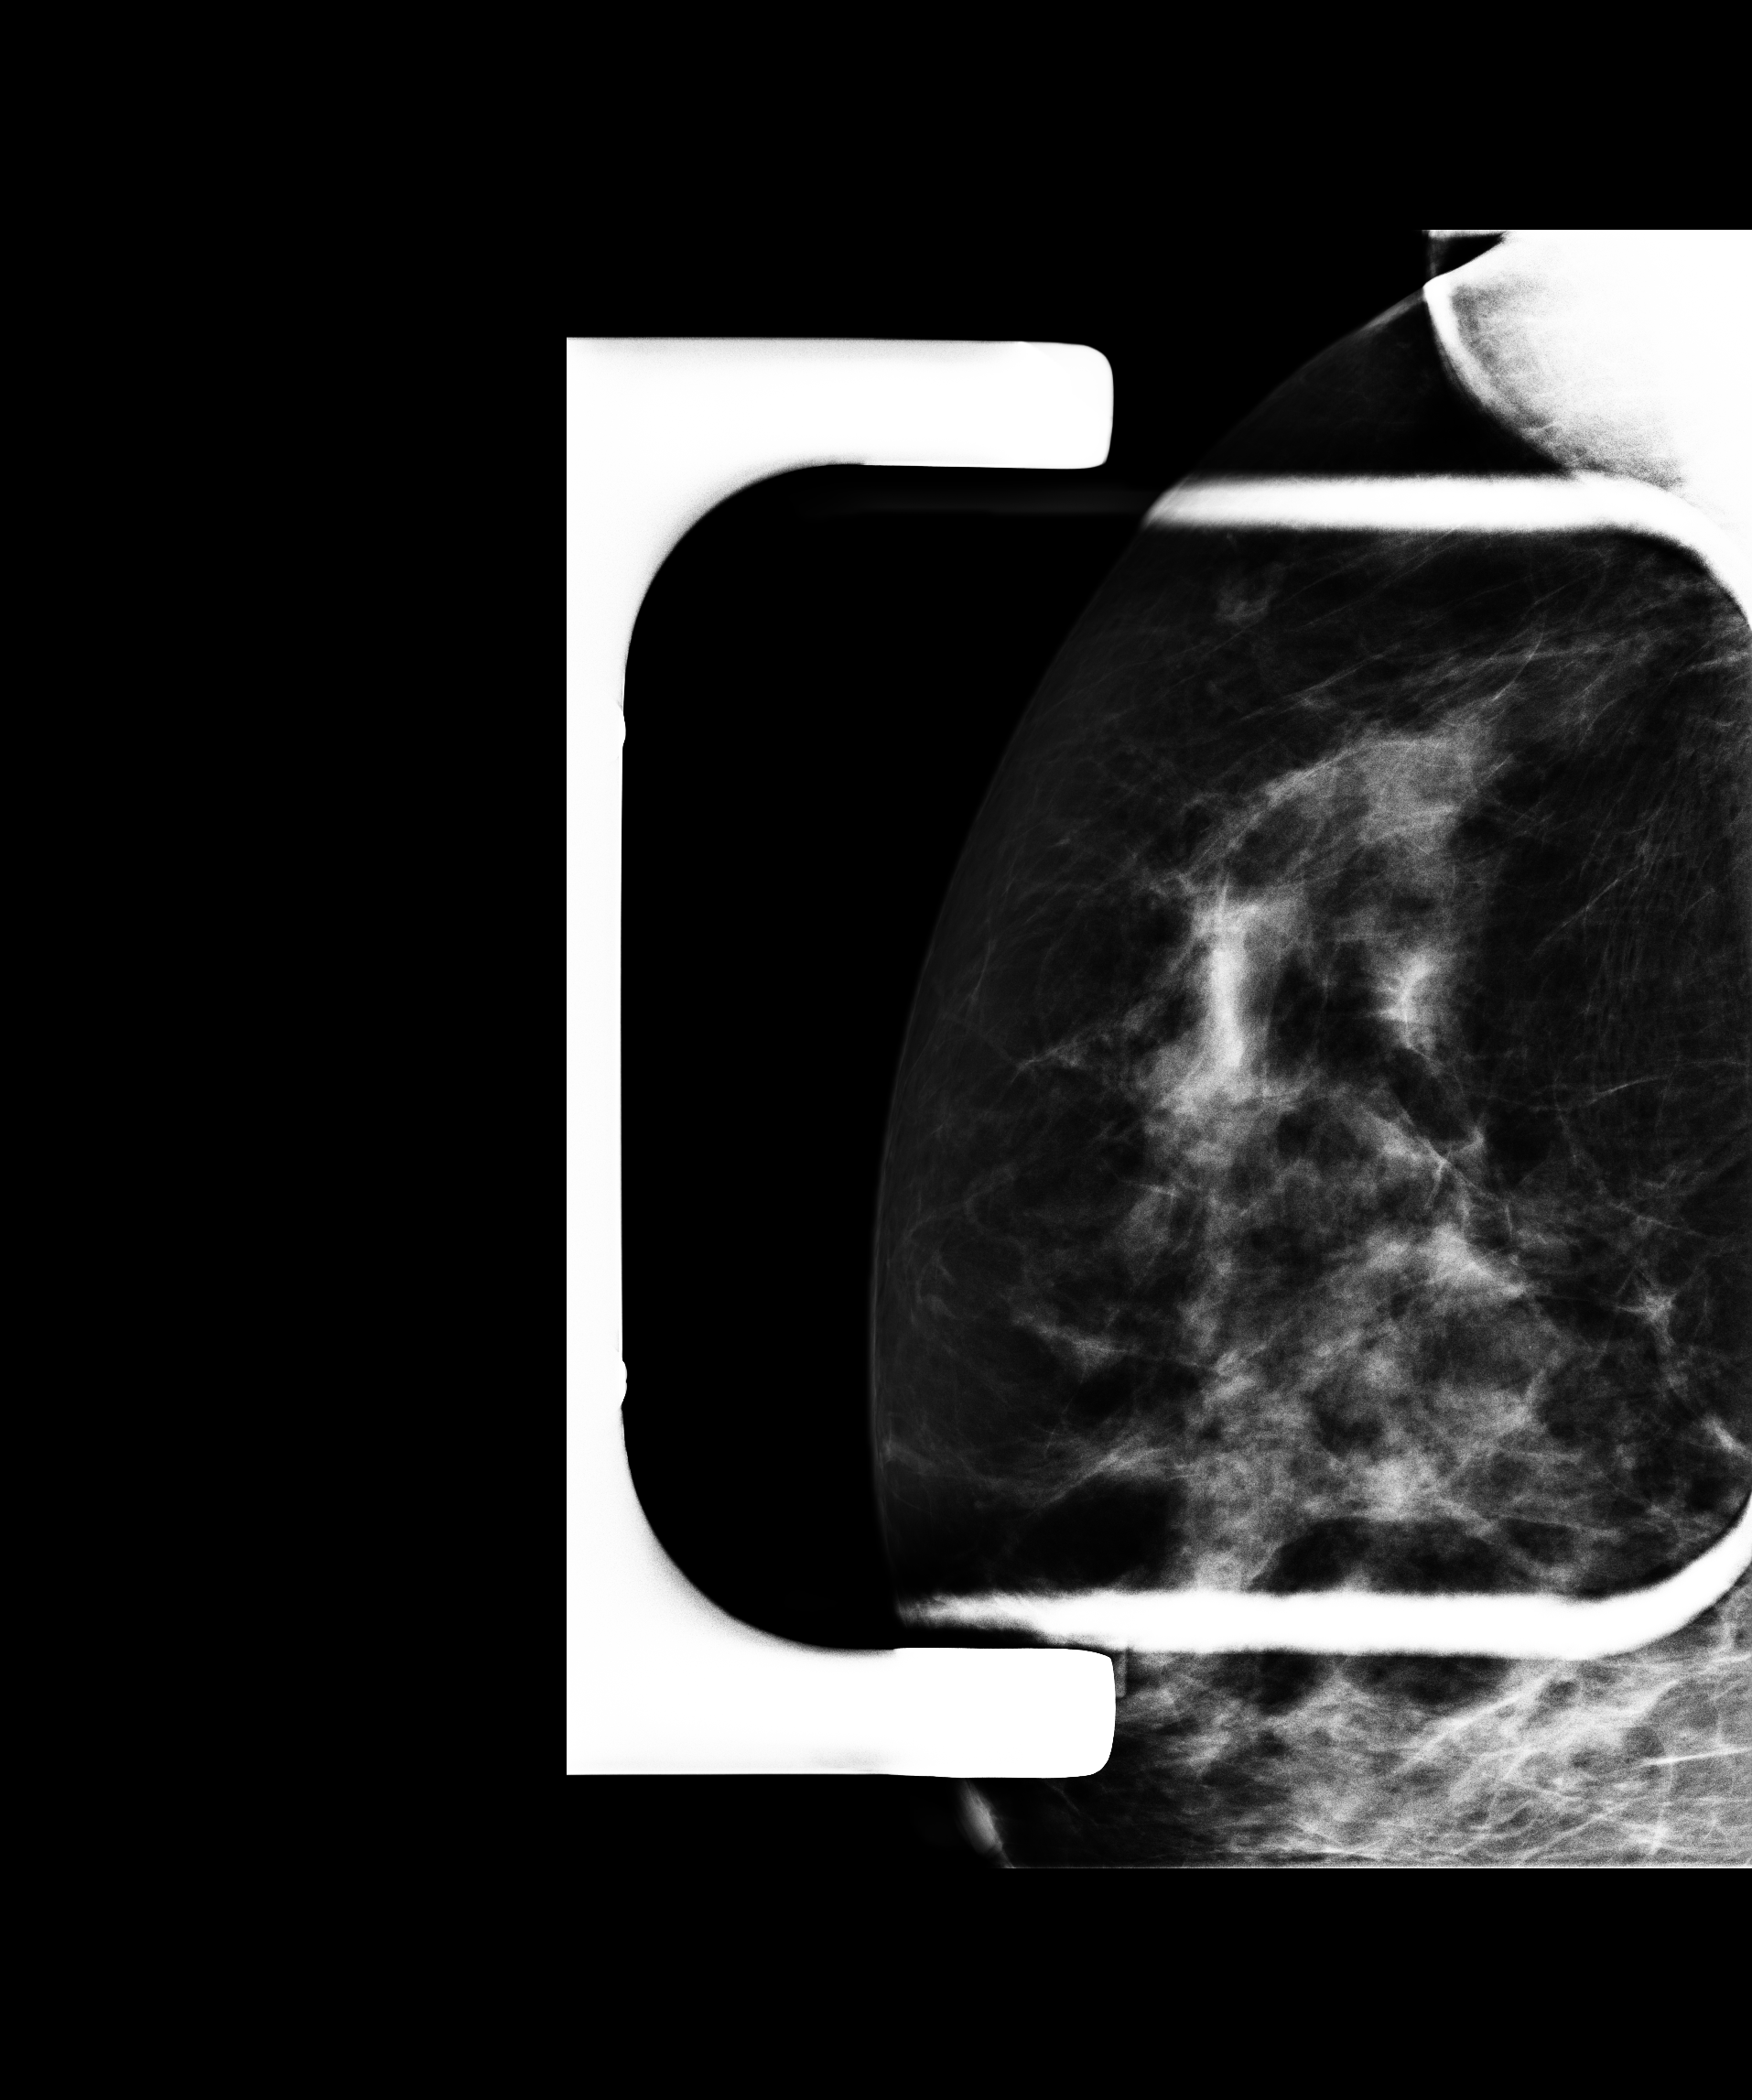
Additional work-up view.
Image type: full-field digital mammogram. Breast: right. Projection: craniocaudal (CC) view, spot compression.